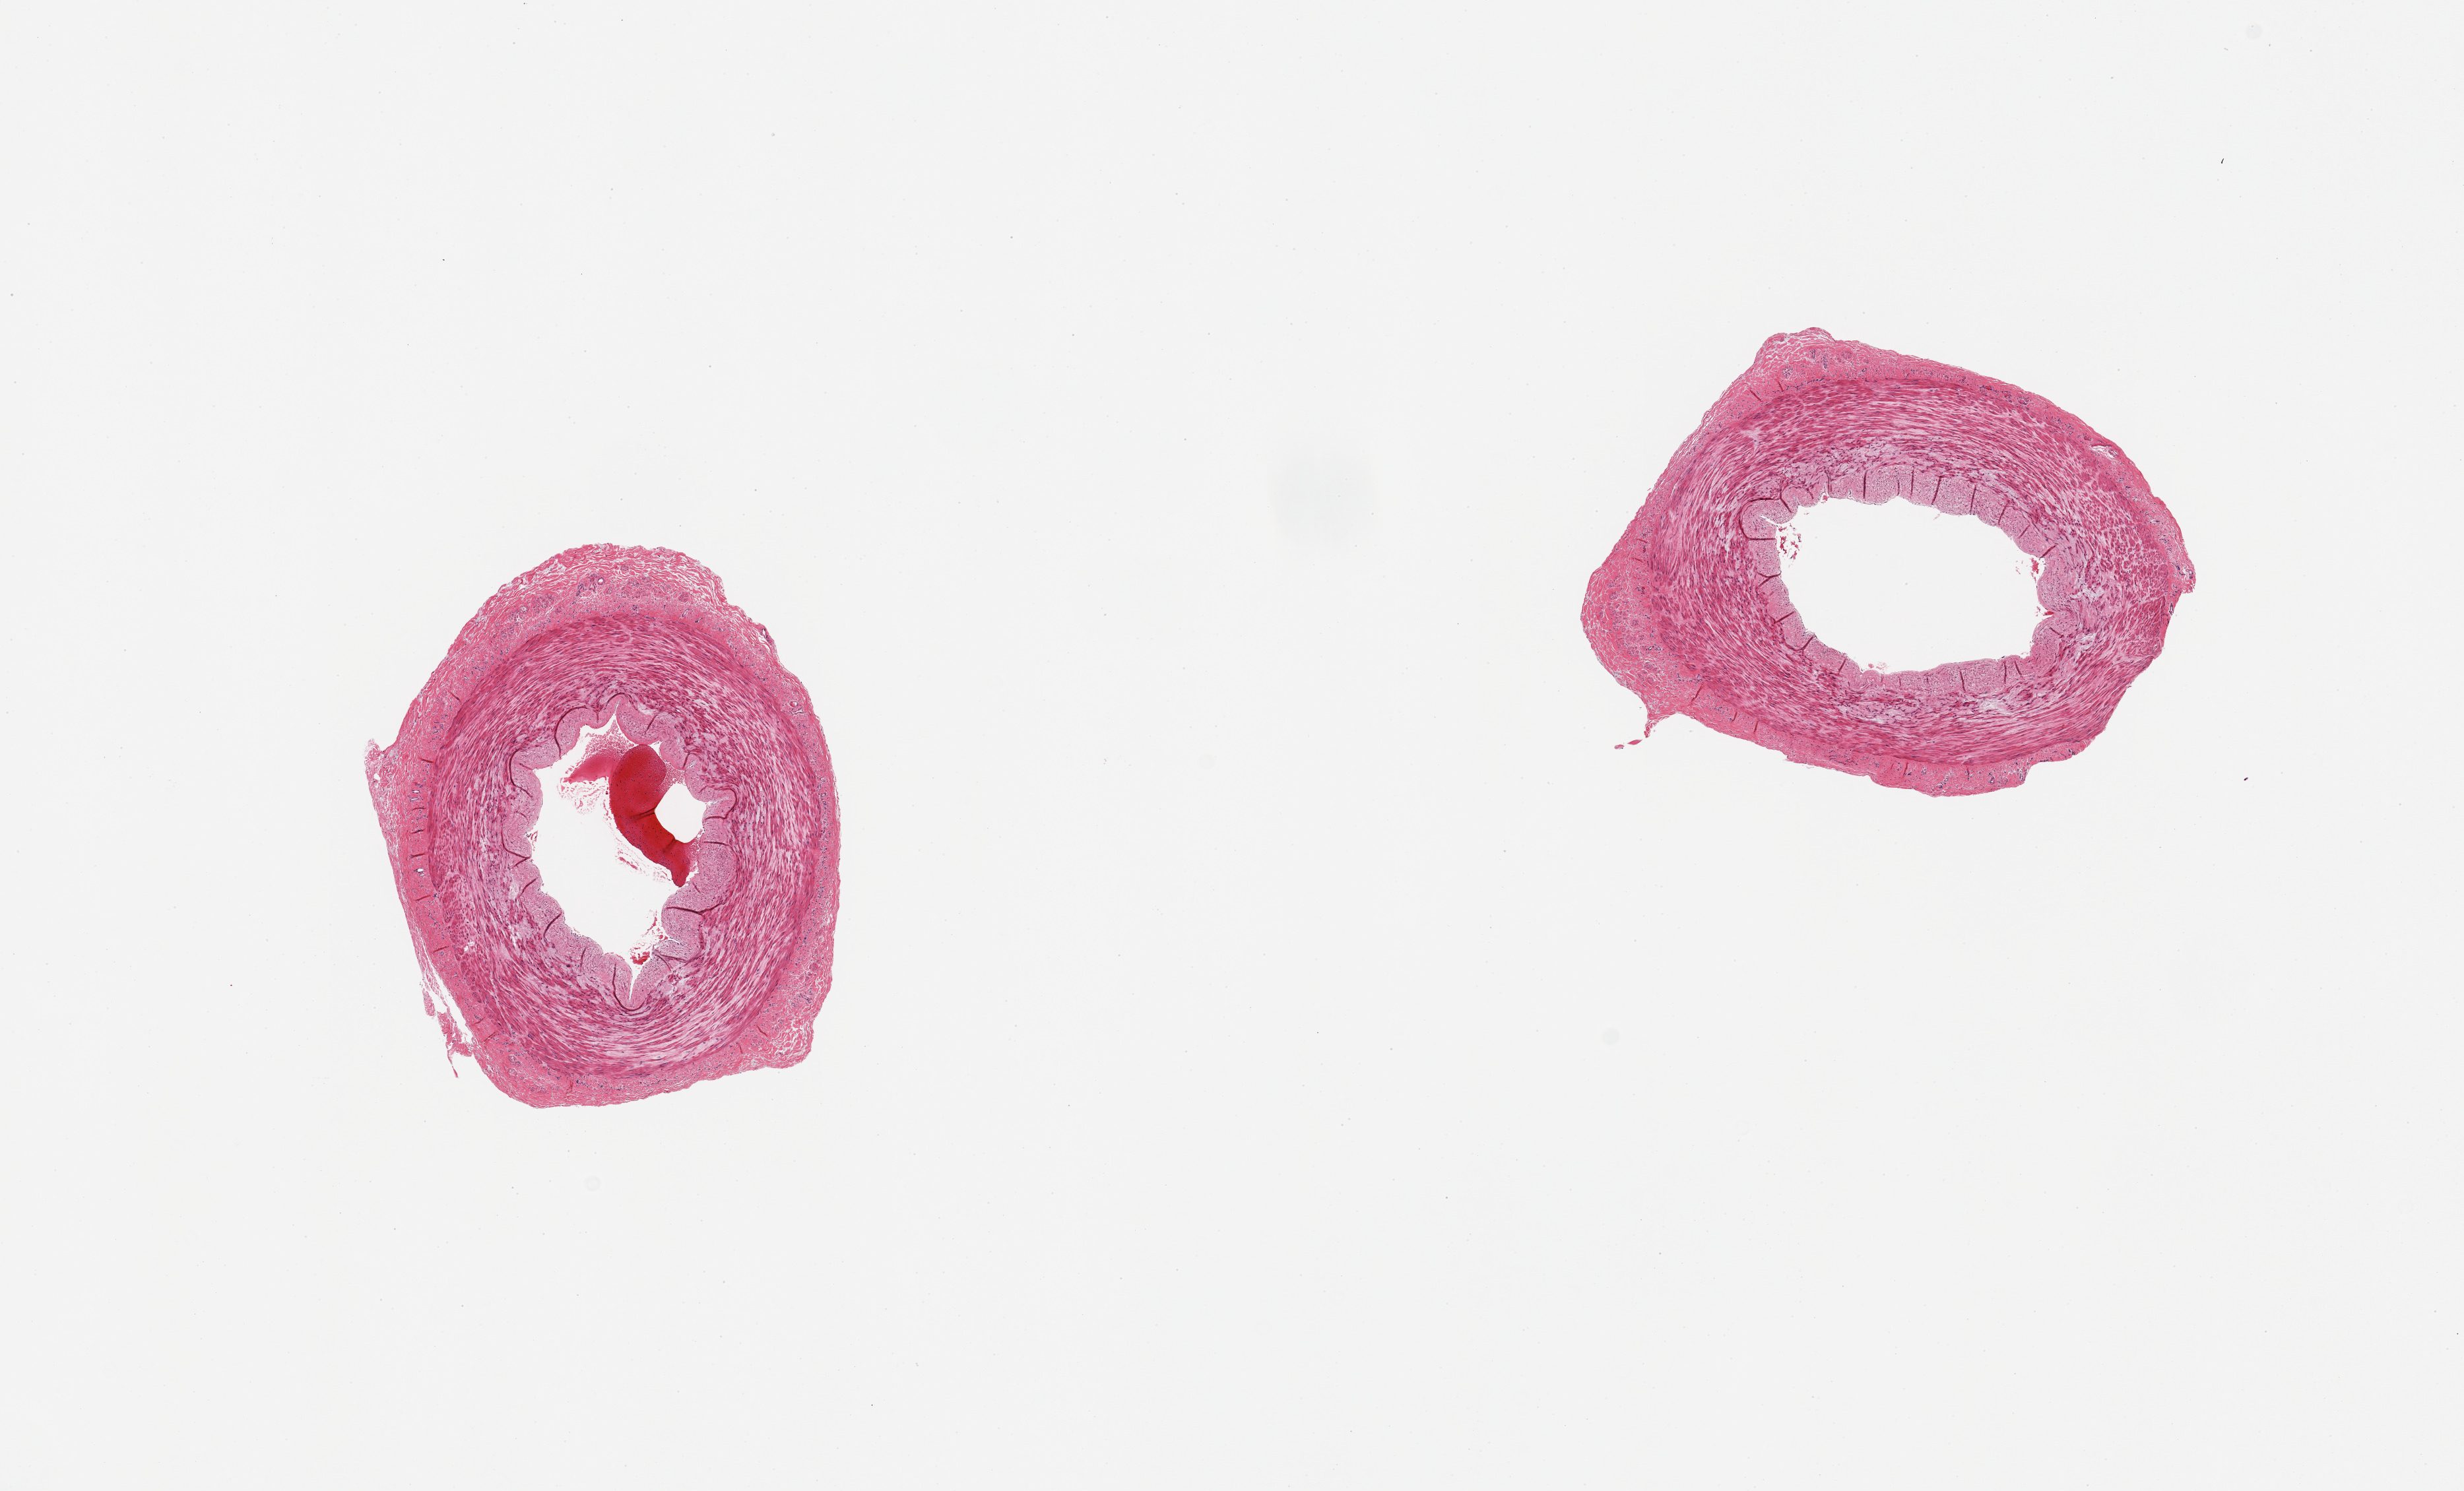
Whole-slide image, hematoxylin and eosin (H&E) stain, a low-resolution overview of the entire scanned area, about 14.8 x 8.9 mm (from a 20x scan). PAXgene-fixed, paraffin-embedded tissue. Target tissue: tibial artery. Donor tissue sample.
Review note (as recorded): 2 pieces, no atherosis, clean specimens.